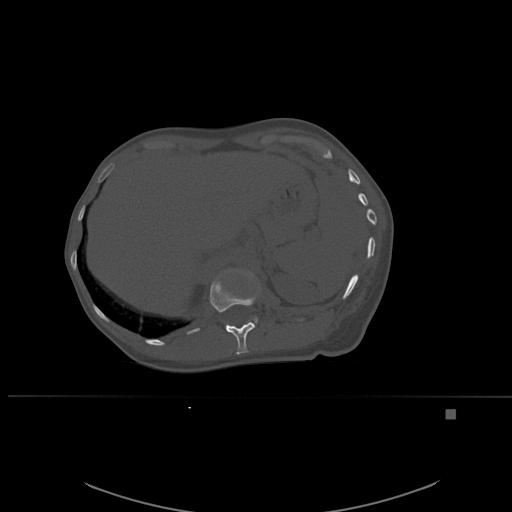
CT including the spine, one axial slice. Position 274 of 537 along the scan axis. Bone window (W 1800 / L 400 HU). 1.5 mm slice thickness. 512 × 512 image matrix, field of view 440 × 440 mm. Patient: female, 45 years. Case-level facts recorded for this patient, not image findings: primary cancer: lung.
Outlined on this slice (semi-automatically segmented with operator editing):
- L1 vertebra: bounding box [x1, y1, x2, y2] px = [225, 269, 258, 328]
- T12 vertebra: [210, 277, 257, 355]